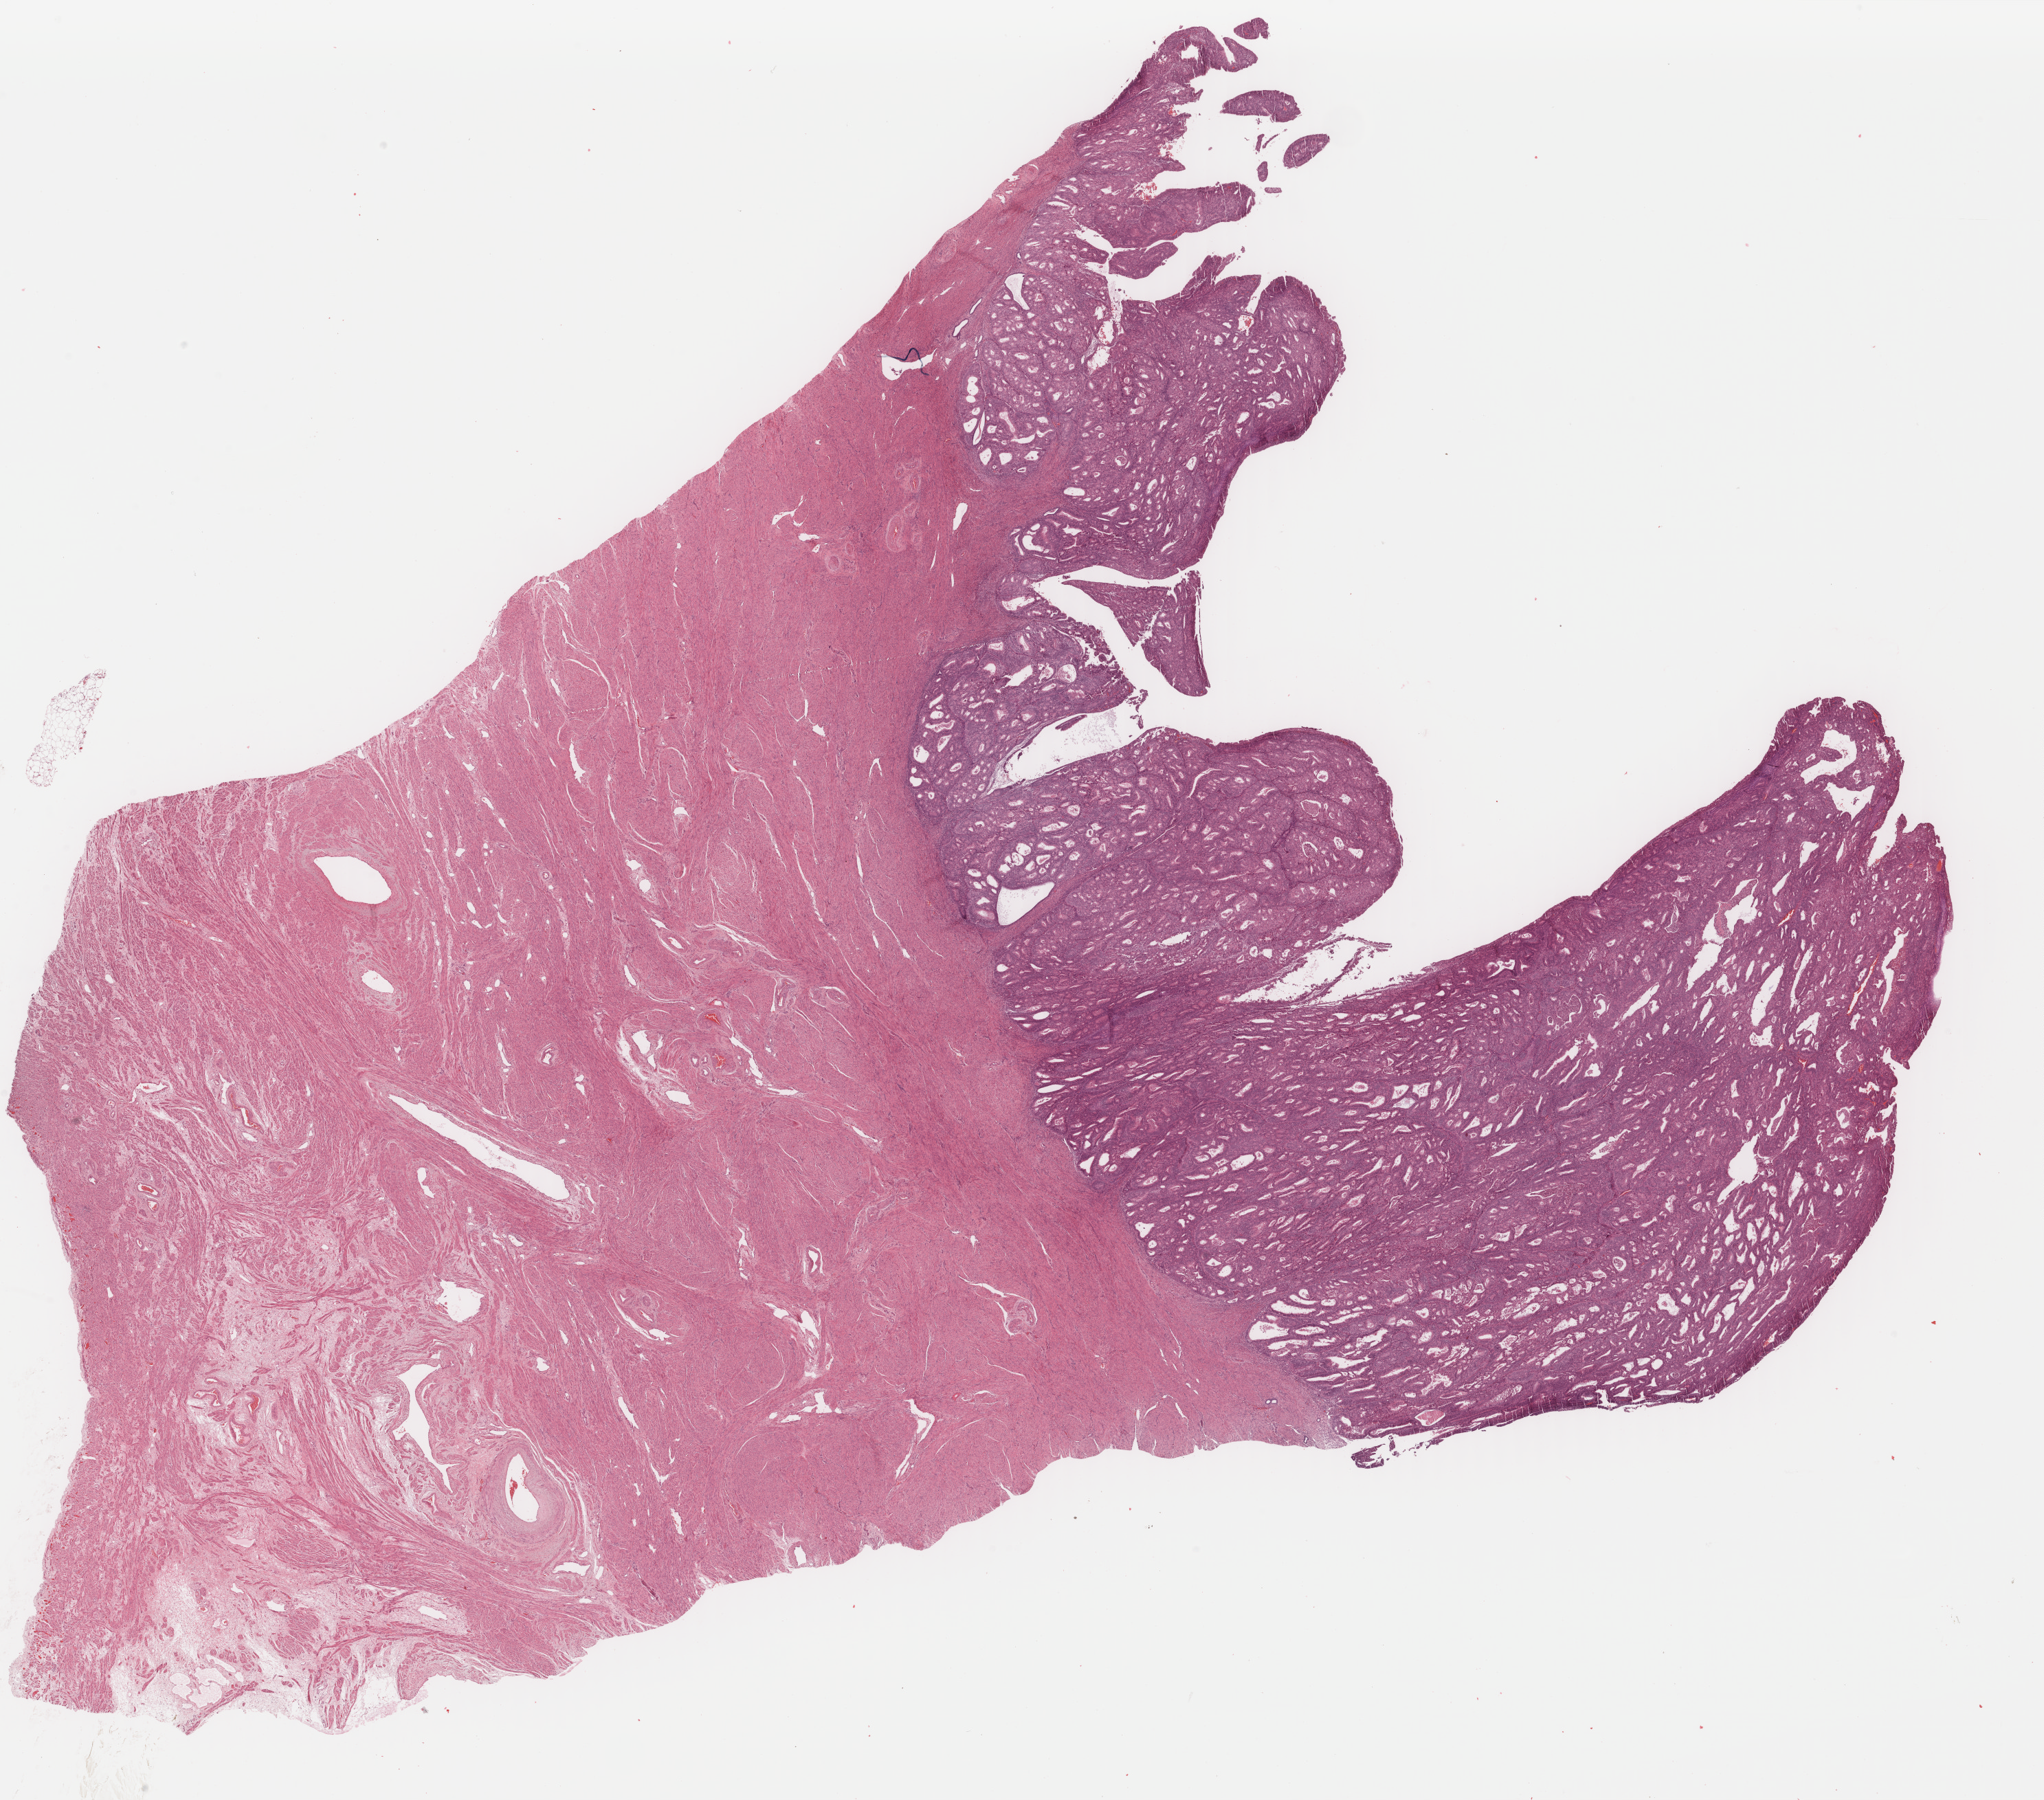
H&E whole-slide image, low-resolution overview of the scanned area, about 23.6 x 20.8 mm (from a 40x scan); formalin-fixed paraffin-embedded (FFPE) diagnostic section; sample: primary tumour, uterus. Patient: female, age at initial diagnosis 76 years. Histologic grade: G1 (well differentiated).
* histologic diagnosis: Endometrioid adenocarcinoma, NOS (endometrium)
* FIGO stage: IA